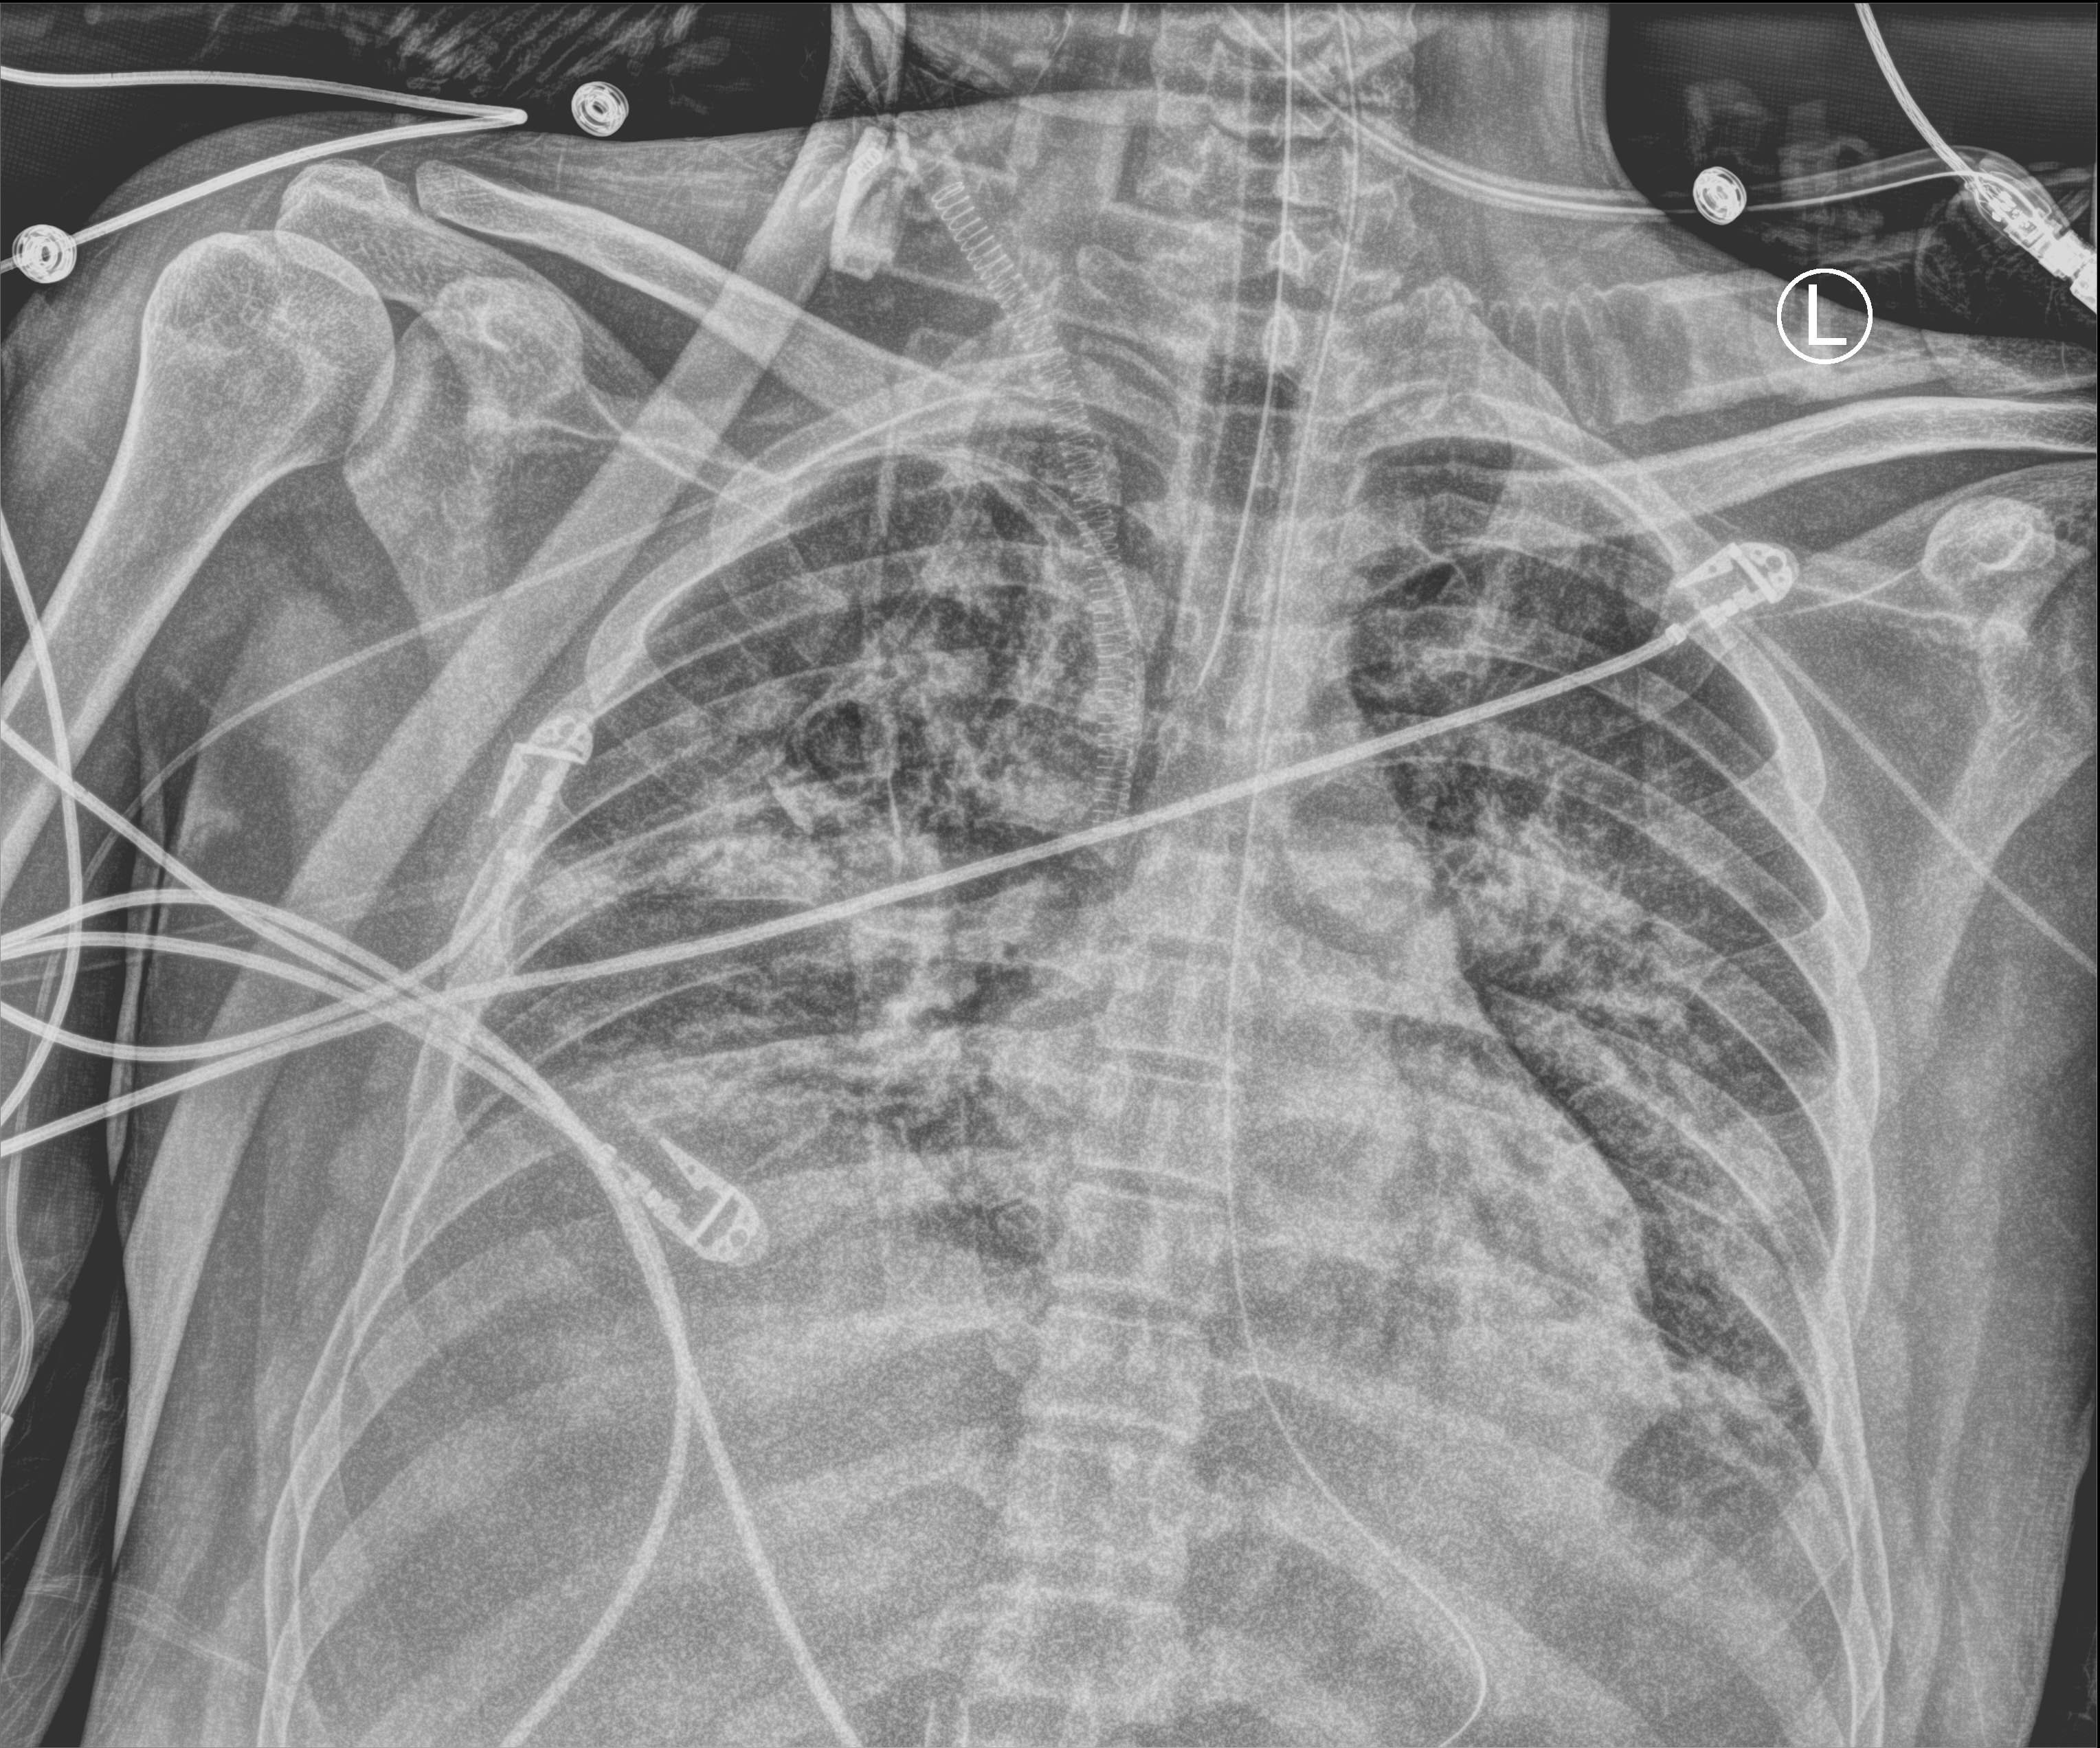
Portable chest radiograph; anteroposterior (AP) projection. Adult patient hospitalised with COVID-19, age 18–59 years.
Hospital-stay facts (about this admission, not read from this image; timing relative to this image not recorded): diabetes (admission record): no; hypertension (admission record): no; mechanically ventilated during this hospital stay: yes.